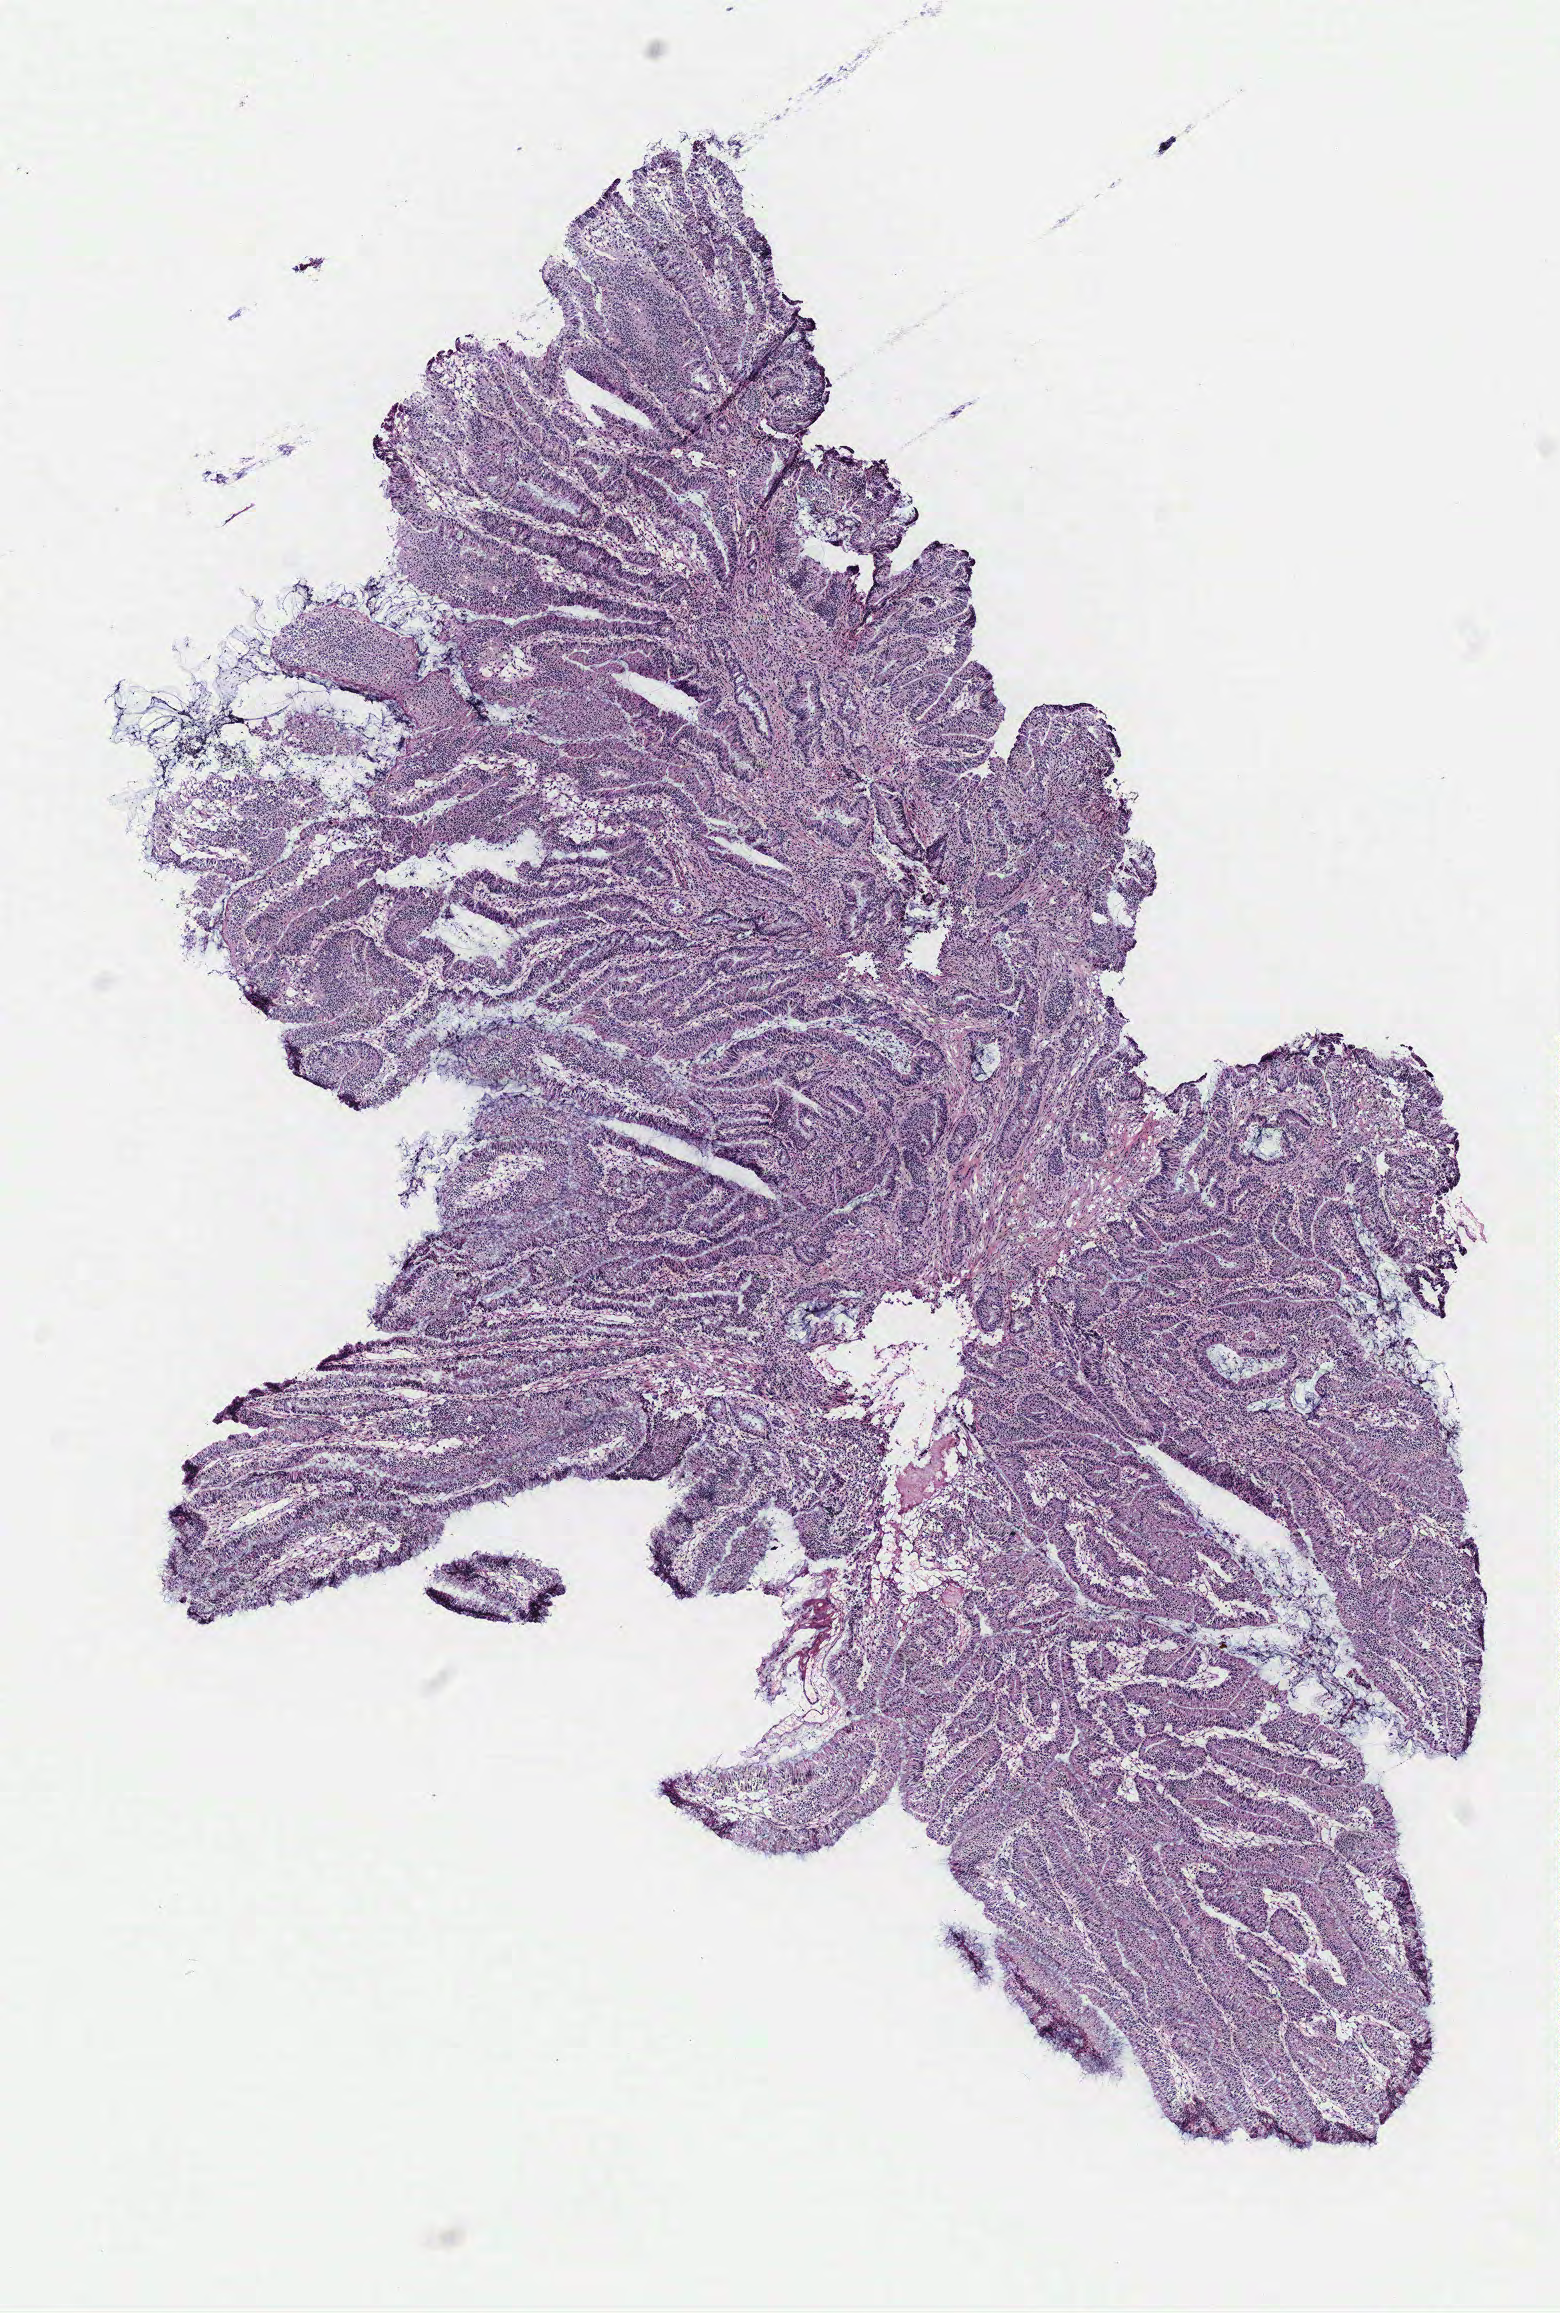
H&E whole-slide image — whole scanned area (about 6.2 x 9.3 mm, slide scanned at 40x) shown as a low-resolution overview. Colon, tissue type not recorded.
- patient diagnosis (cohort enrolment): colon cancer (colon)